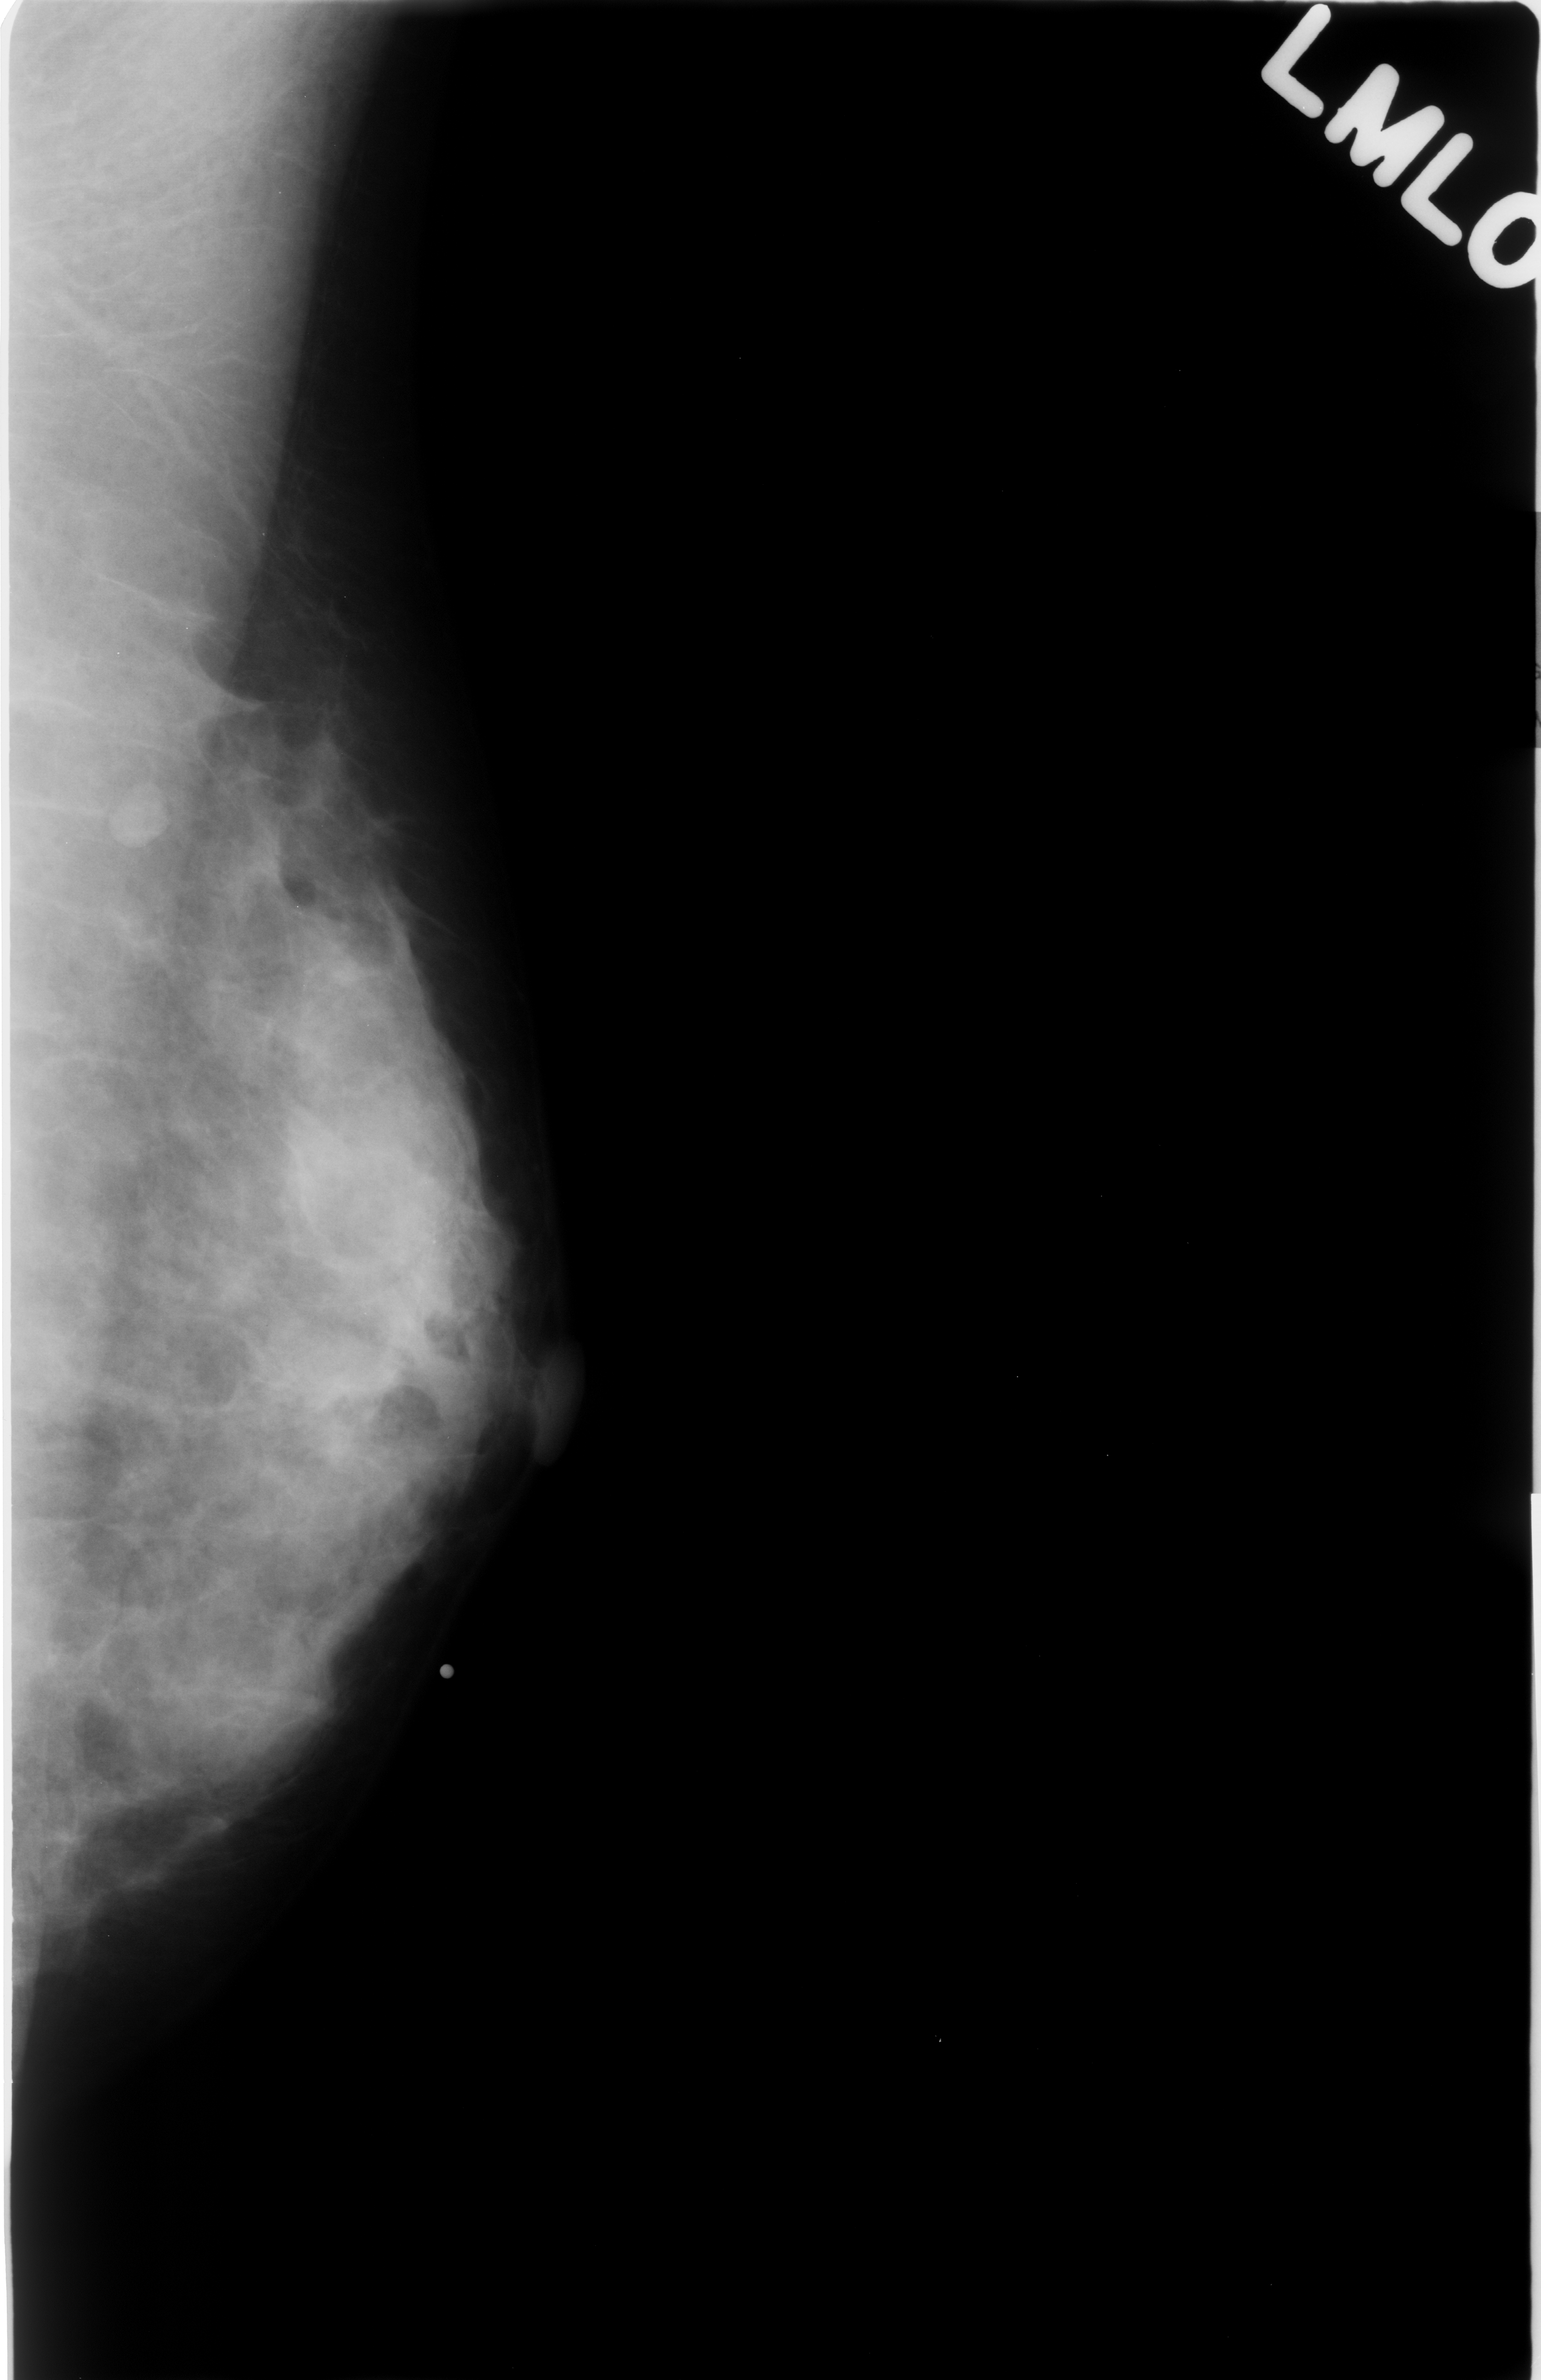
Mammogram (digitized film); left breast; MLO view; breast composition: heterogeneously dense (BI-RADS density category 3 of 4).
Abnormality record for this image: mass, shape round, margins obscured; BI-RADS assessment category 4; subtlety rating 2 on a 1 (subtle) to 5 (obvious) scale; pathology result (as recorded, not read from the image): benign.